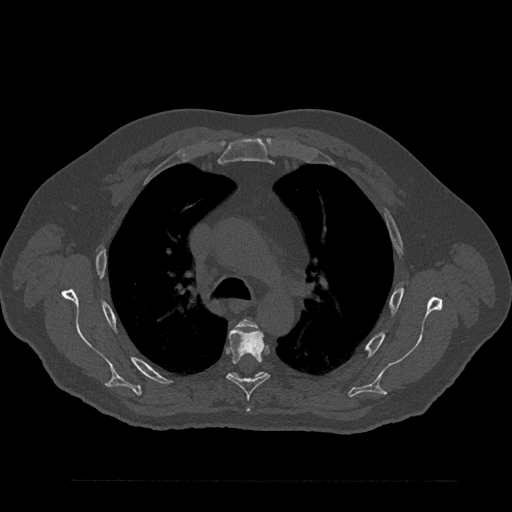
CT including the spine, one axial slice; slice 601 of 797 in the series (ordered by position); bone window (W 1800 / L 400 HU); 0.5 mm slice thickness; 512 × 512 image matrix, field of view 430 × 430 mm. Male patient, age 61 years. From the clinical record (not read from this slice): primary cancer: prostate.
Annotated regions visible in this slice (semi-automatically segmented with operator editing):
- T4 vertebra: bounding box (x1, y1, x2, y2) in pixels: (239, 319, 256, 327)
- T5 vertebra: (227, 328, 270, 400)
- T6 vertebra: (230, 372, 266, 380)